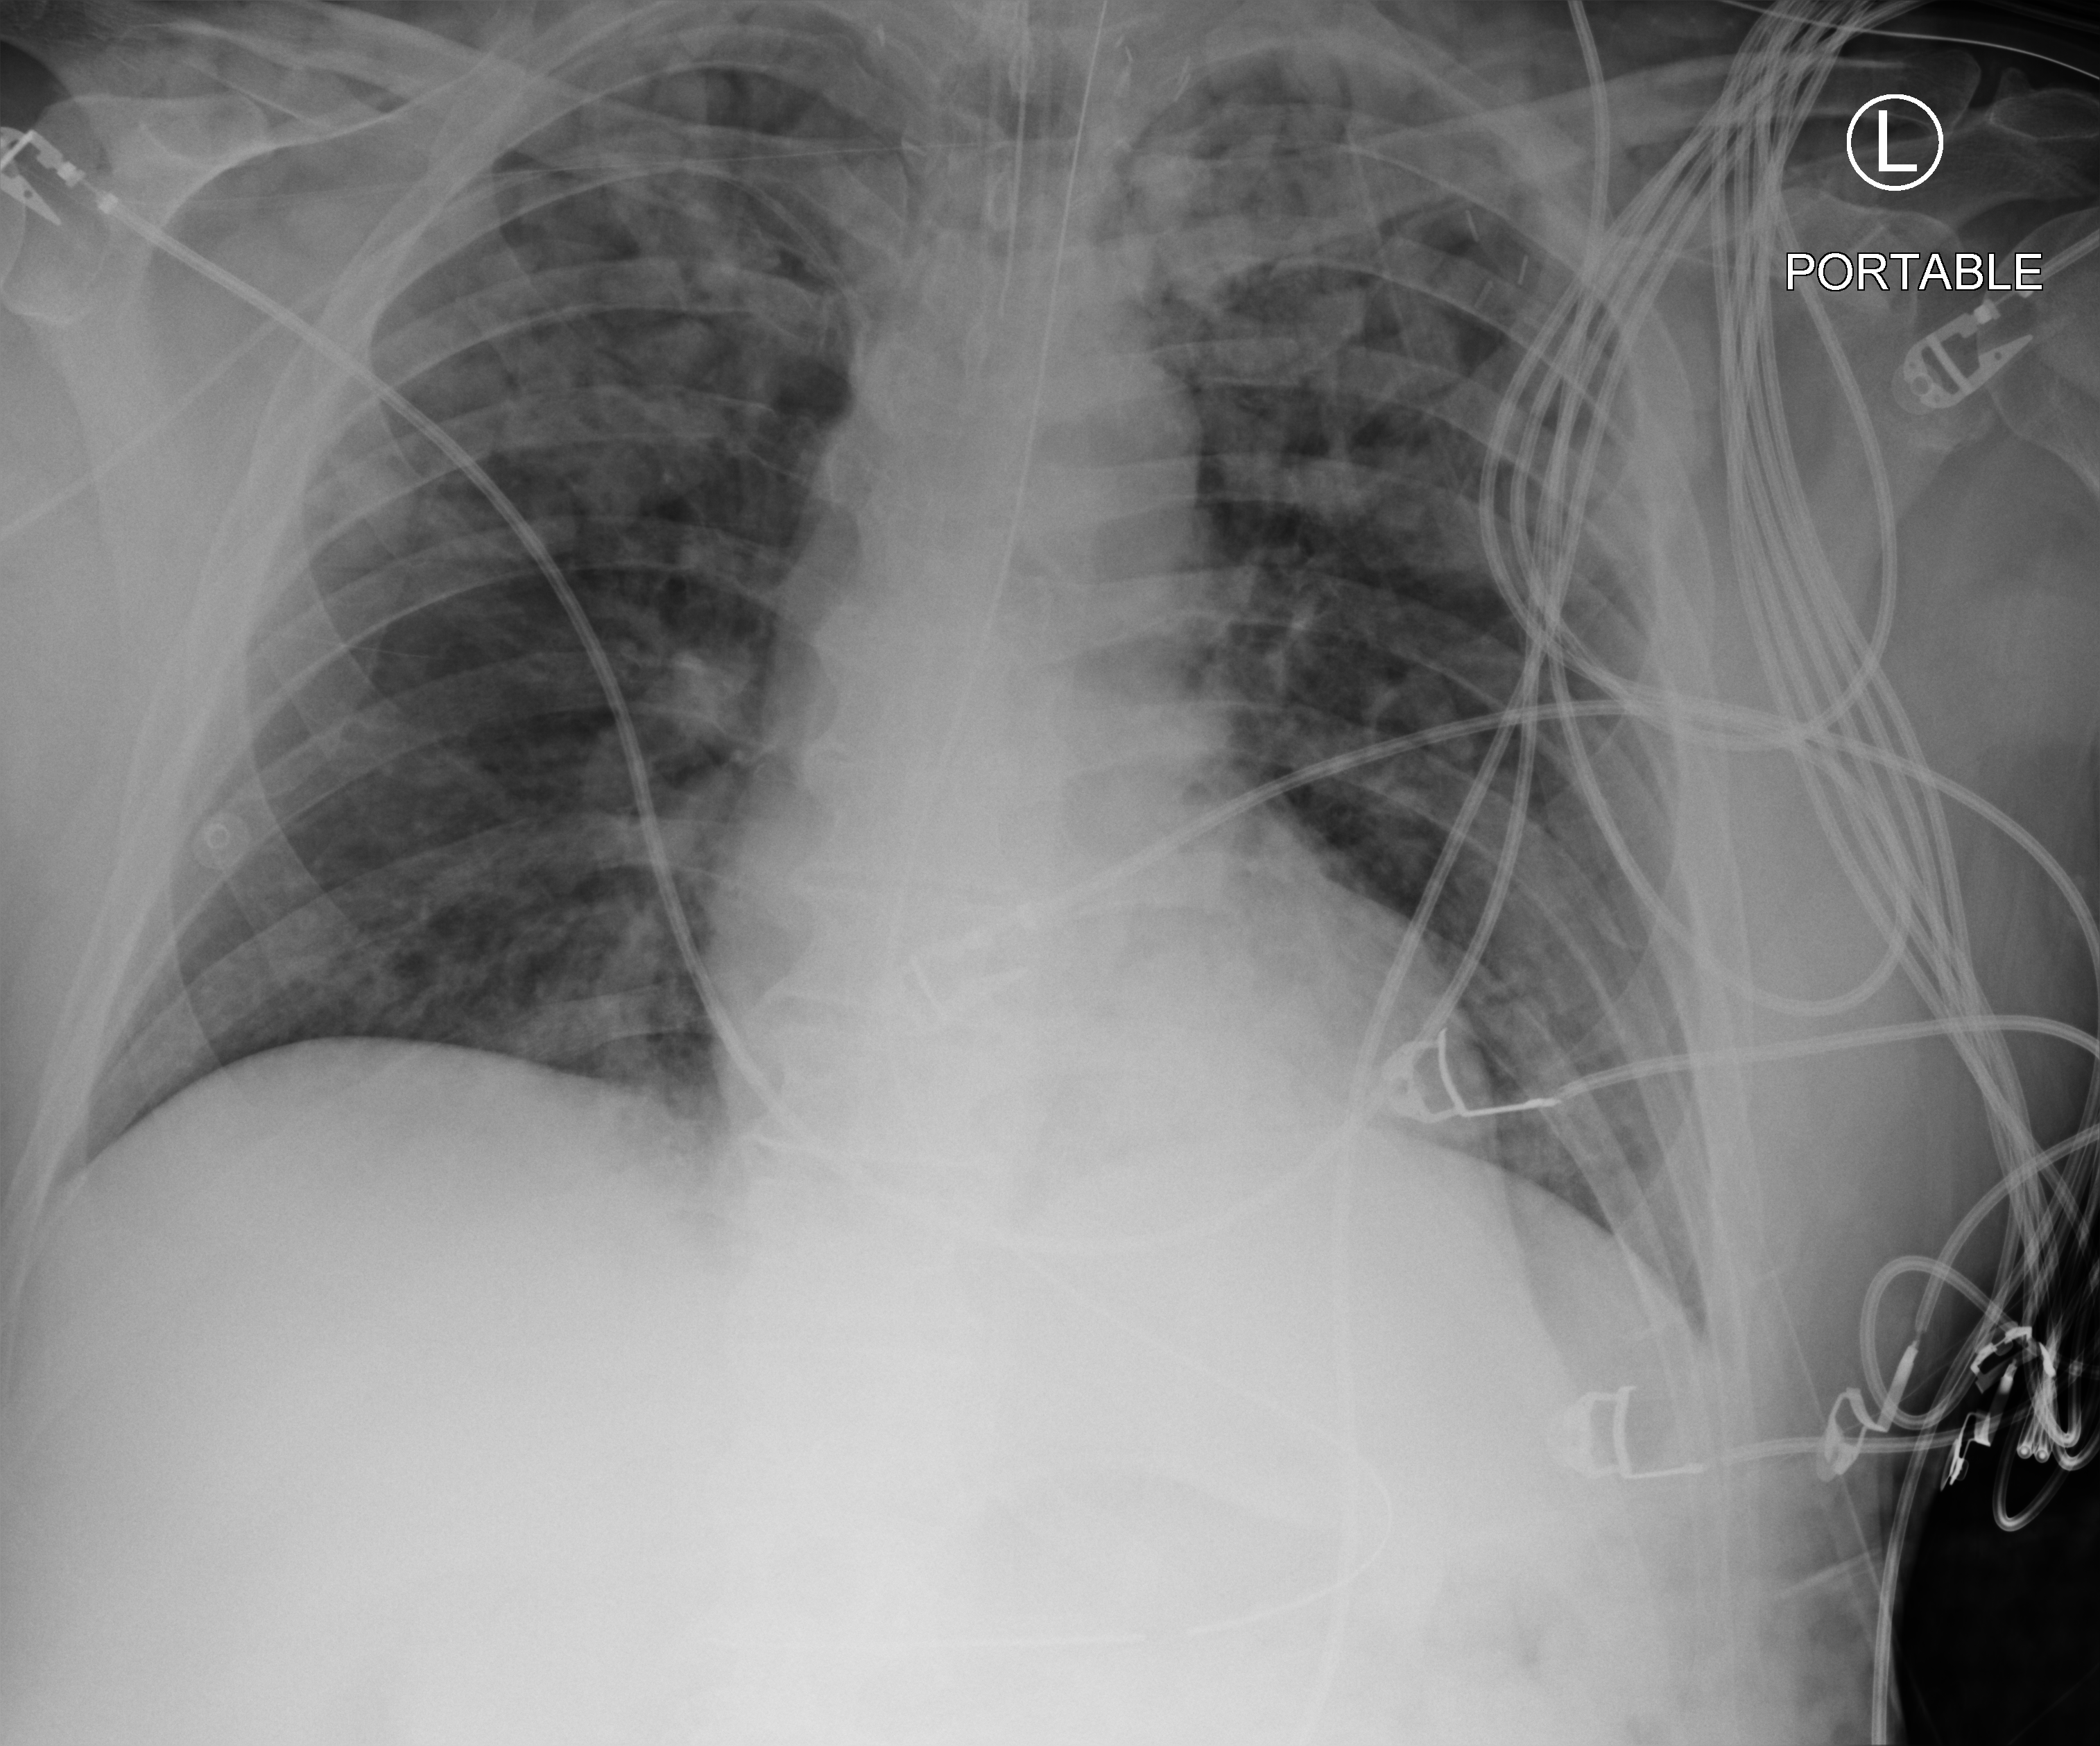
Chest X-ray (portable), anteroposterior (AP) projection. Patient hospitalised with COVID-19, aged 18–59 years.
From the hospital-stay record, not from the radiograph (when in the stay this image was taken is not recorded):
- diabetes (admission record): yes
- admitted to intensive care during this hospital stay: yes
- mechanically ventilated during this hospital stay: yes